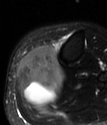
MRI of an extremity soft-tissue mass, one axial slice; position 27 of 78 along the scan axis; T2-weighted fat-saturated; MR volume resampled by the dataset authors to the PET/CT grid (not the native acquisition matrix); 3.27 mm slice thickness; 107 × 125 image matrix. Female patient. From the clinical record (not read from this slice): histological type: extraskeletal high grade osteogenic sarcoma; grade: high; site of the primary tumour: left calf.
Annotated regions visible in this slice (expert contour drawn on MRI and transferred to this co-registered scan by the dataset authors):
- gross tumour volume (mass): bounding box (x1, y1, x2, y2) in pixels: (16, 47, 63, 106)